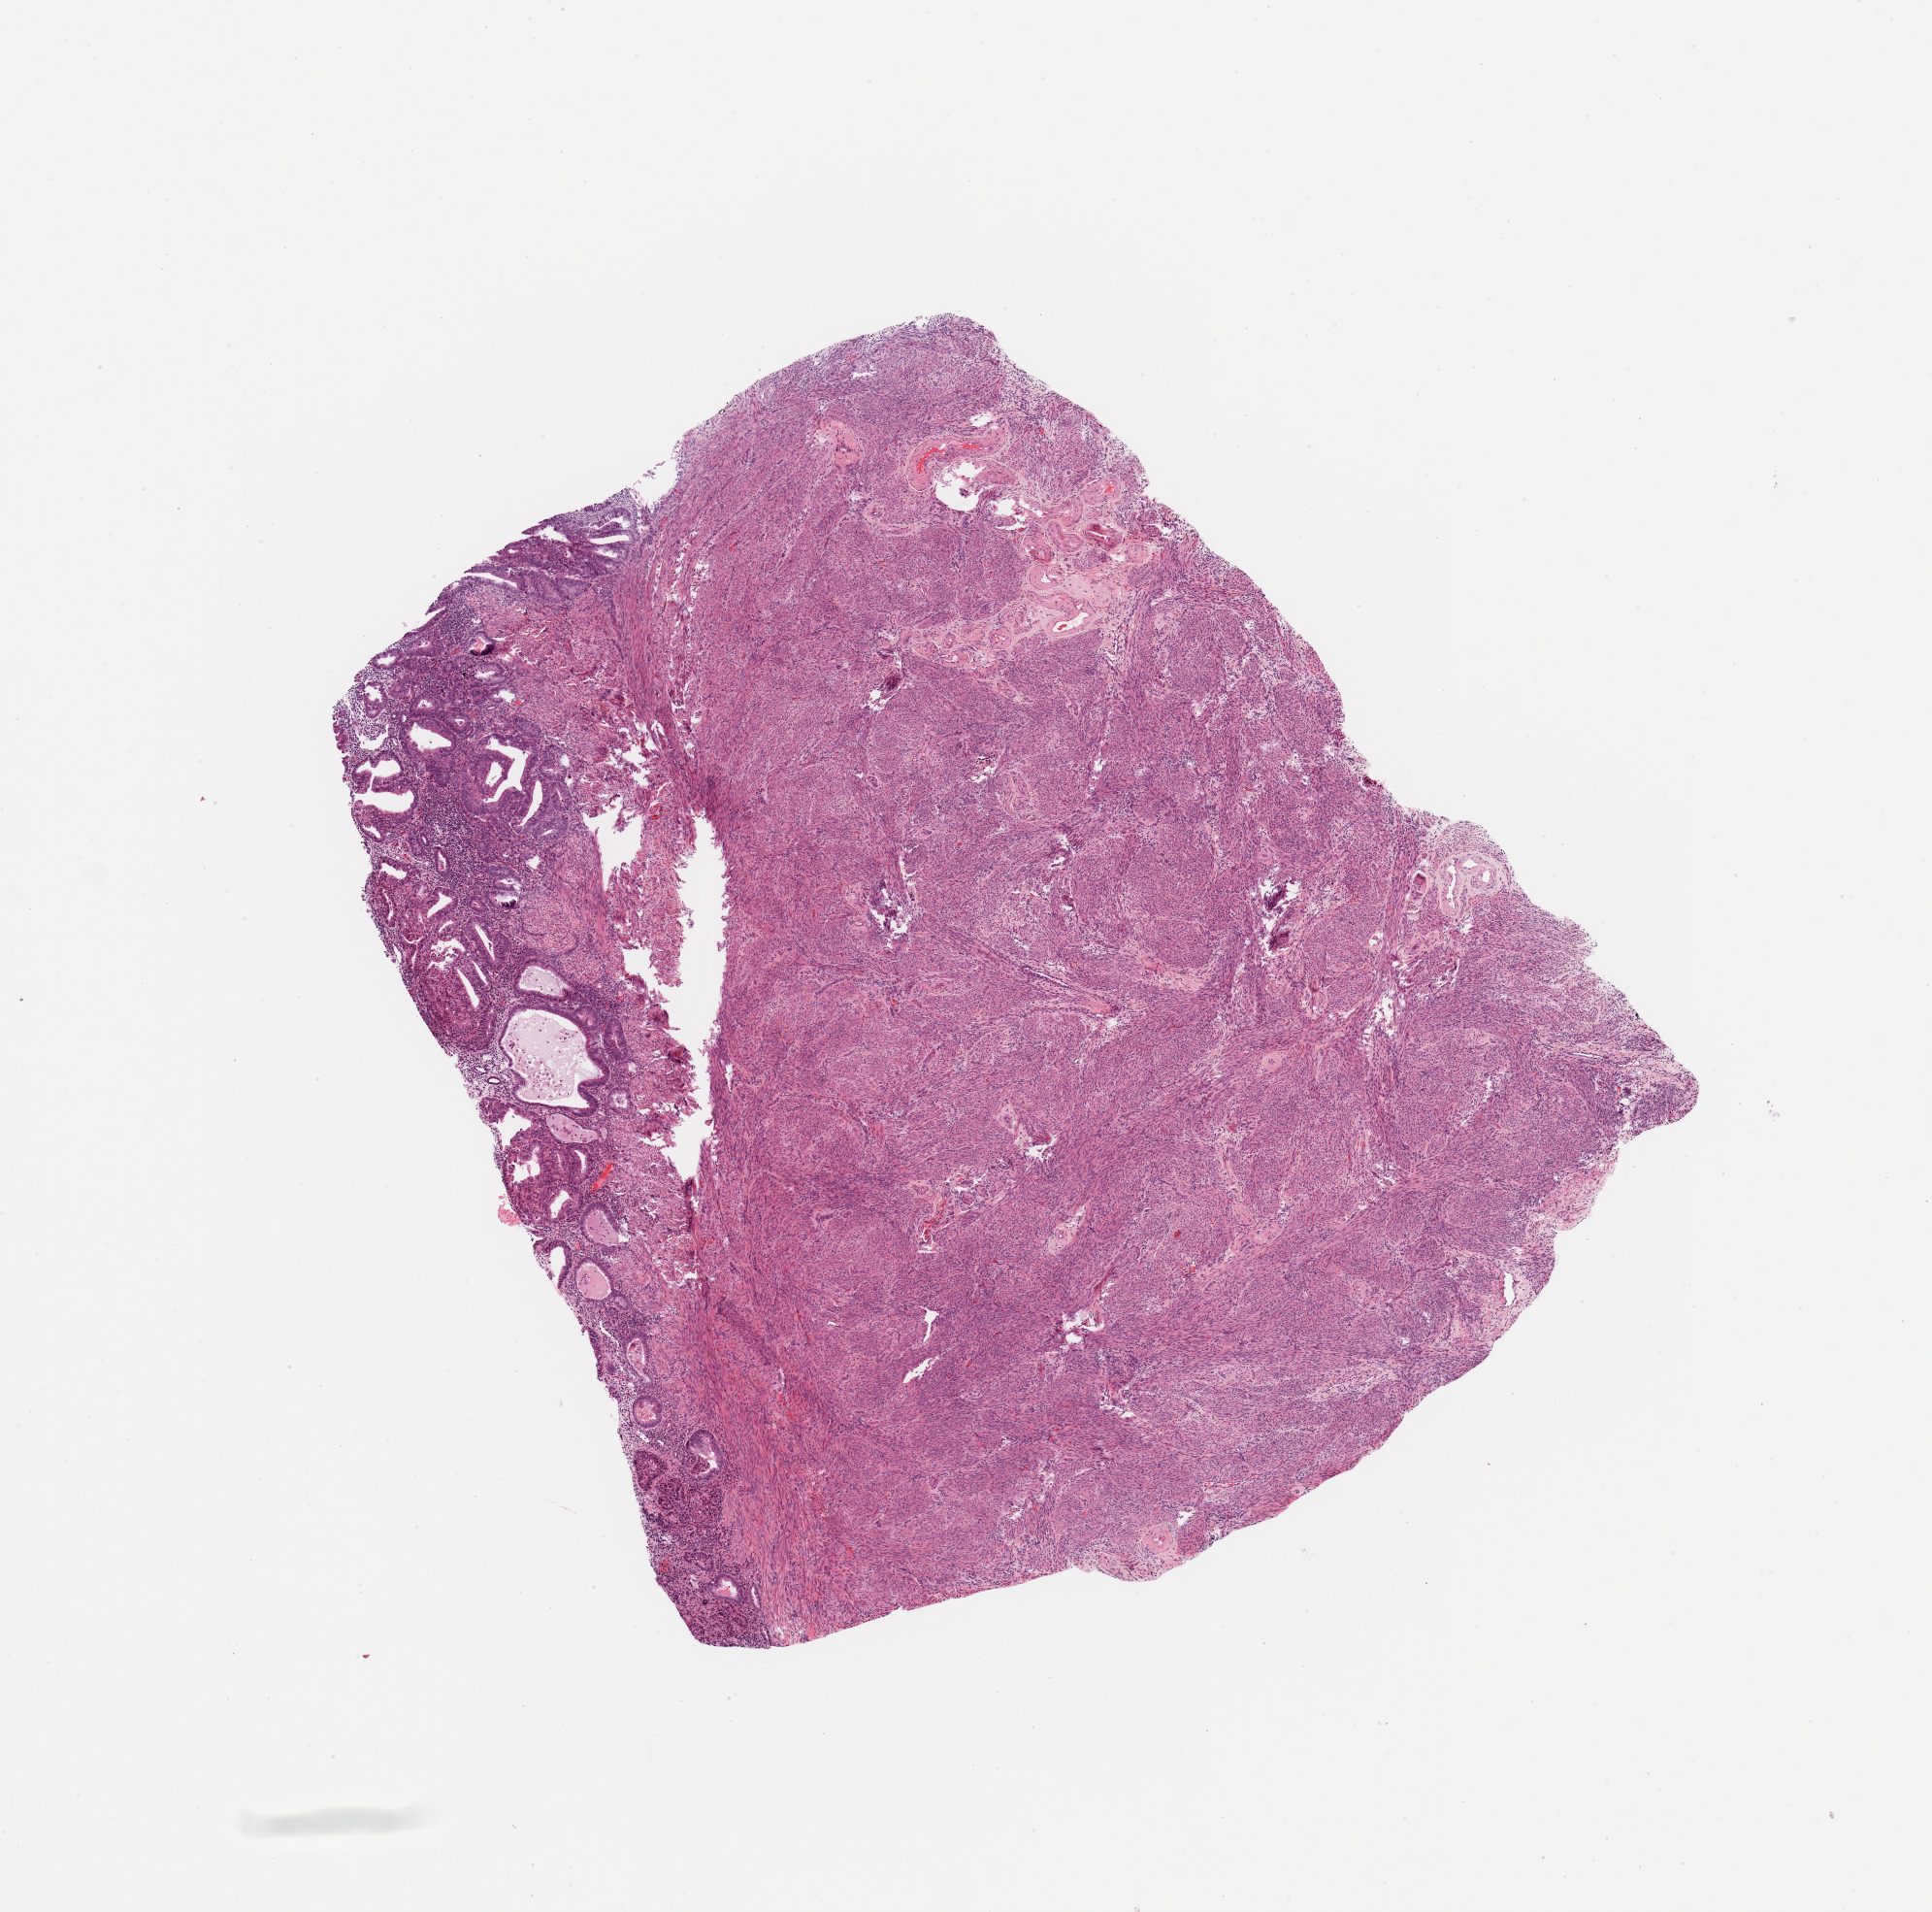
Hematoxylin and eosin (H&E) stained whole-slide image, shown as a low-resolution overview of the whole scanned area (about 7.9 x 7.8 mm, slide scanned at 20x), normal (non-tumour) tissue sample, sampled site: uterus. 62-year-old female patient.
This section: normal (non-tumour) tissue from the same patient. Patient diagnosis: Endometrioid adenocarcinoma, NOS.